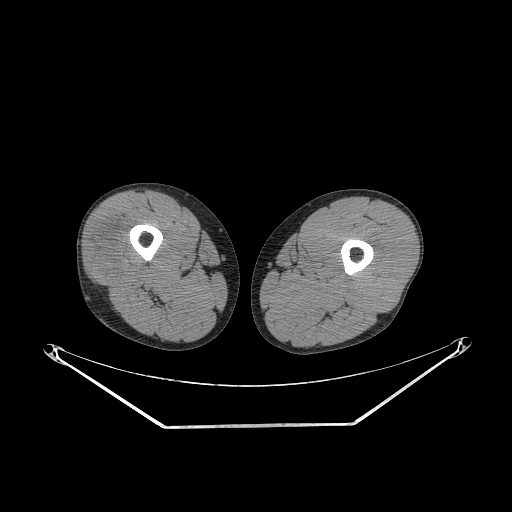
CT of an extremity soft-tissue mass (from a PET/CT study), one axial slice. Reconstruction kernel STANDARD. Soft-tissue window (W 400 / L 40 HU). 512 × 512 image matrix. Male patient. Case-level facts recorded for this patient, not image findings: histological type: poorly differentiated synovial sarcoma; grade: high; site of the primary tumour: right buttock.
Annotated regions visible in this slice (expert contour drawn on MRI and transferred to this co-registered scan by the dataset authors):
- gross tumour volume including surrounding oedema: bounding box (x1, y1, x2, y2) in pixels: (91, 230, 138, 280)